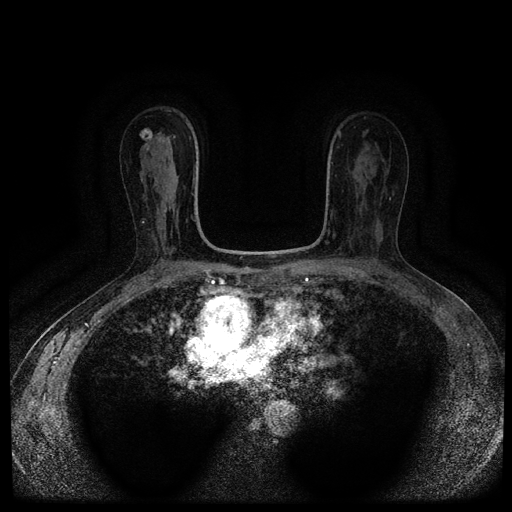
Breast MRI (dynamic contrast-enhanced, multi-phase), one axial slice. Position 62 of 116 along the scan axis. Dynamic contrast-enhanced series, time point 2 of 5 at this slice position (early post-contrast). 1.5 T. TE 2.7 ms, TR 5.4 ms. 2 mm slice thickness. 512 × 512 image matrix, field of view 330 × 330 mm. Female patient, age 63 years.
Structures marked on this image (semi-automatic segmentation, software-assisted and operator-edited):
- breast lesion (labelled benign in the annotation): bounding box [x1, y1, x2, y2] px = [139, 128, 153, 144]